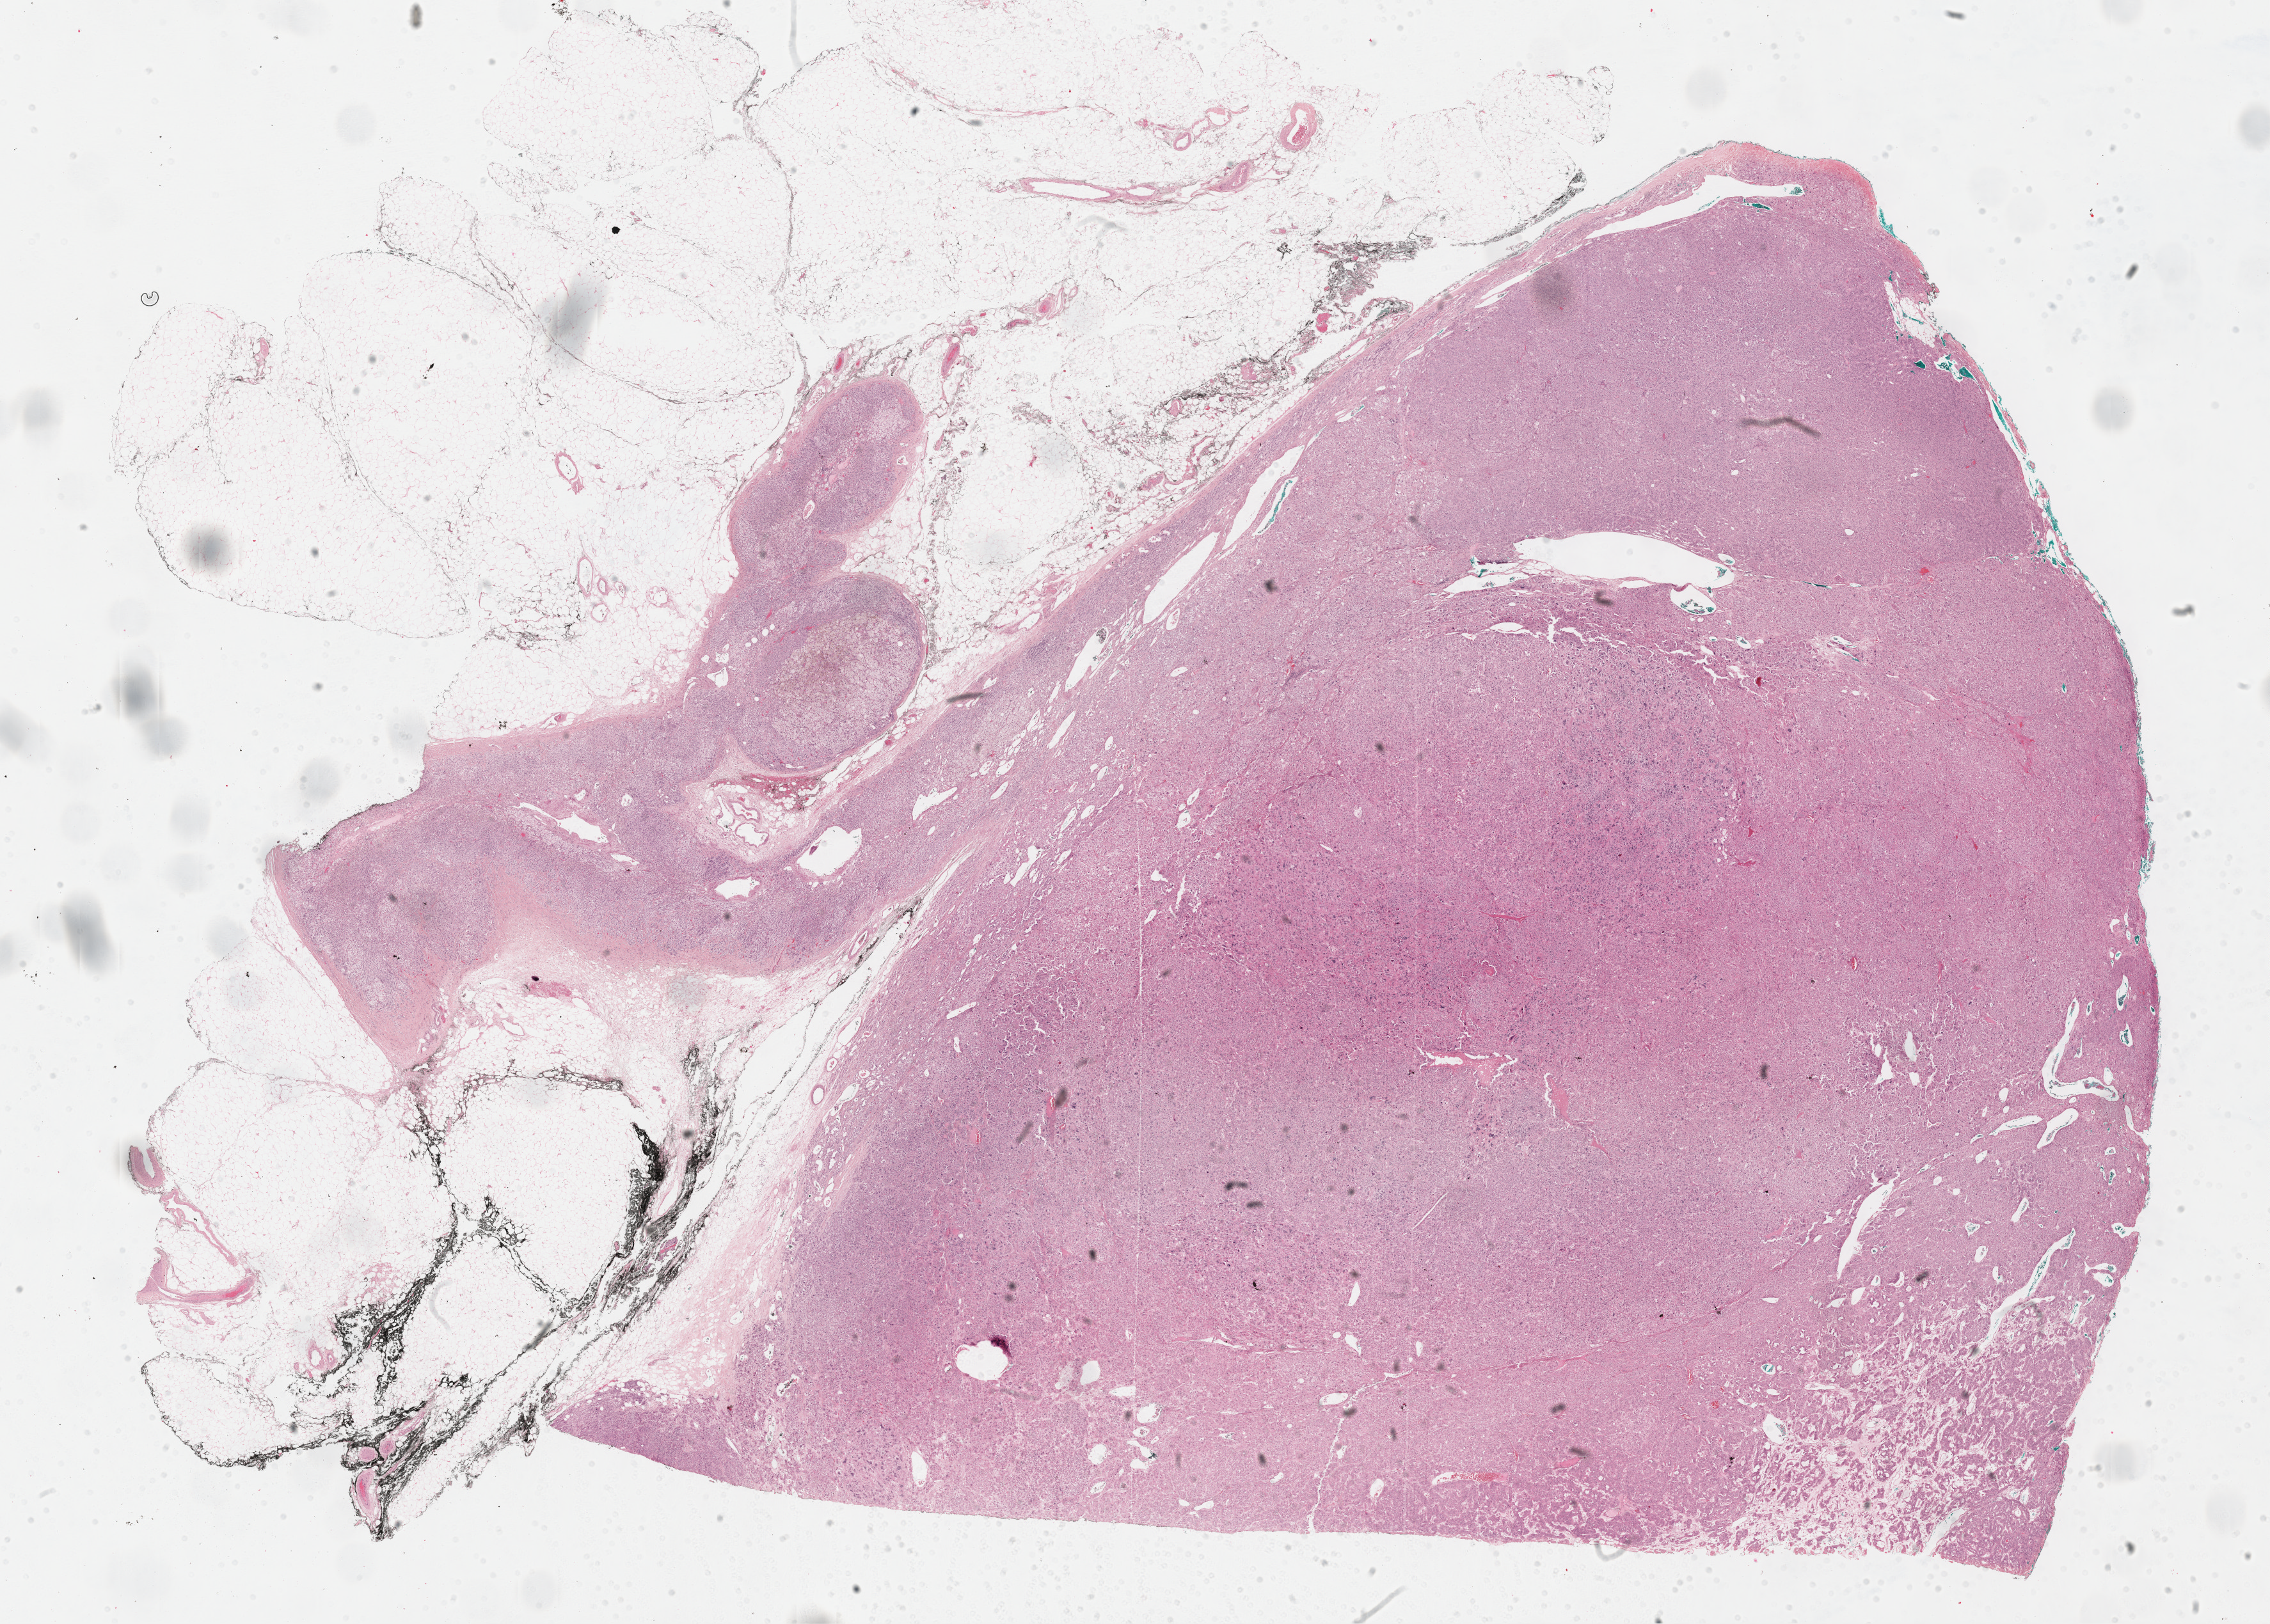
Digitized H&E-stained tissue section (whole slide) — low-resolution overview of the scanned area, about 28.7 x 20.5 mm (acquisition: 40x scan), FFPE section, sample: primary tumour, adrenal cortex. Female patient; age at initial diagnosis 69 years.
Histologic diagnosis: Adrenal cortical carcinoma (cortex of adrenal gland). Laterality: left.